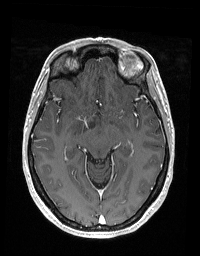
Brain MRI from a brain-tumour surgery series, one axial slice. Slice 110 of 192 in the series (ordered by position). T1-weighted post-contrast. 1 mm slice thickness. 200 × 256 image matrix, field of view 195 × 250 mm. Case-level facts recorded for this patient, not image findings: histopathology: Glioblastoma; WHO grade: 2; IDH mutation: no; tumour location: Right Skull Base Temporal.
Annotated regions visible in this slice (outlined manually by an expert reader):
- tumour: bounding box (x1, y1, x2, y2) in pixels: (88, 123, 94, 128)